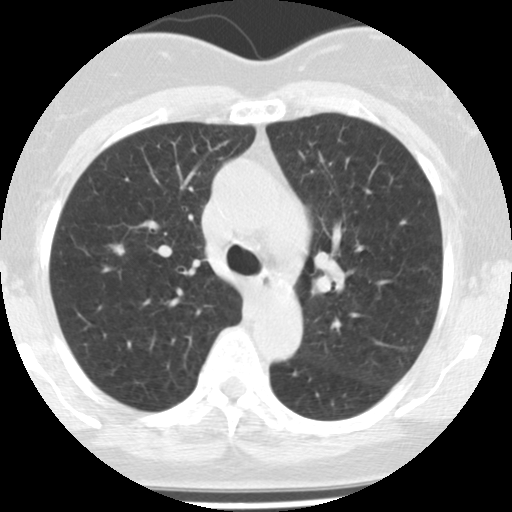
Axial slice from a low-dose chest CT screening exam. First (baseline) screen. Lung window (W 1500 / L -600 HU). 2.5 mm slice thickness. Standard (soft-tissue) reconstruction kernel (STANDARD). Slice 35 of 113 in the series. 512 × 512 image matrix. Female participant, aged 62 years at enrolment. Former smoker at enrolment.
- Expert reader's lesion annotation, bounding box [x1, y1, x2, y2] px = [92, 232, 139, 274].
- No non-calcified nodule or mass ≥4 mm was recorded by the screening reader at this exam.
- Lung cancer was diagnosed 865 days after this screen: adenocarcinoma, NOS, right upper lobe, well differentiated (G1), stage IA (AJCC 6th edition), 7 mm at pathology.